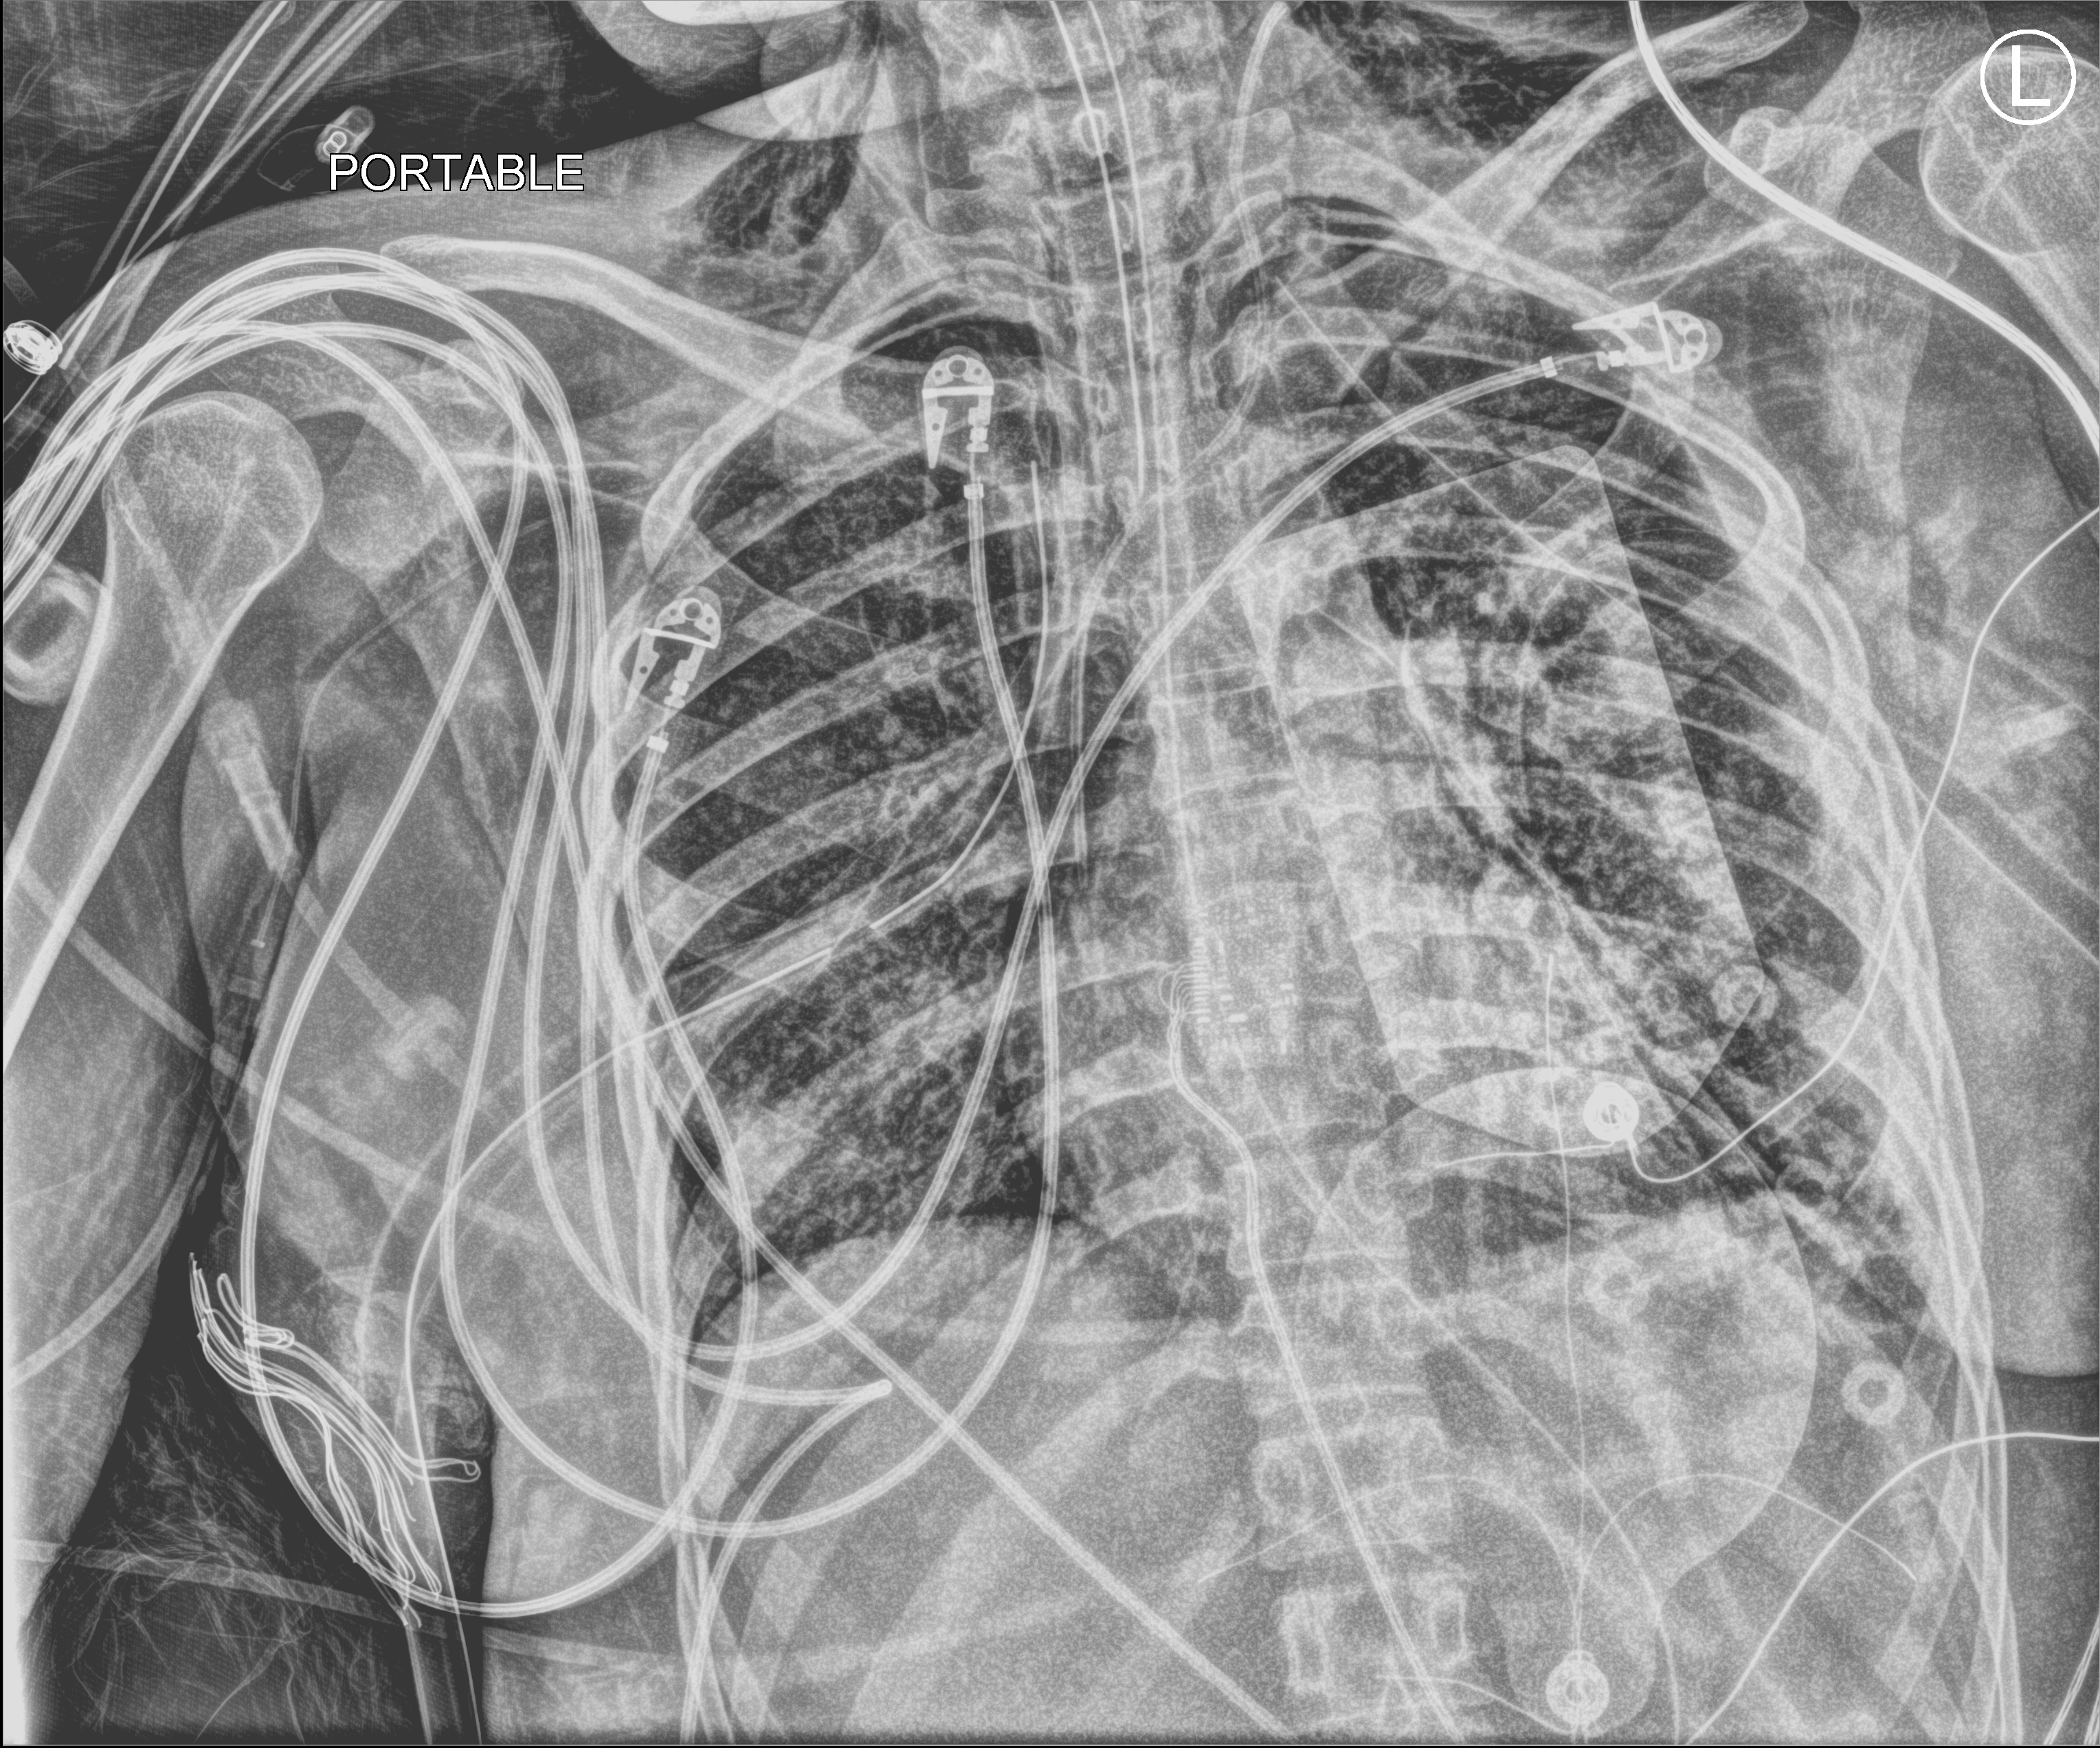
Bedside chest radiograph (computed radiography); anteroposterior (AP) projection. Adult patient hospitalised with COVID-19, age 18–59 years.
Hospital-stay facts (about this admission, not read from this image; timing relative to this image not recorded): COPD (admission record): no; admitted to intensive care during this hospital stay: yes.